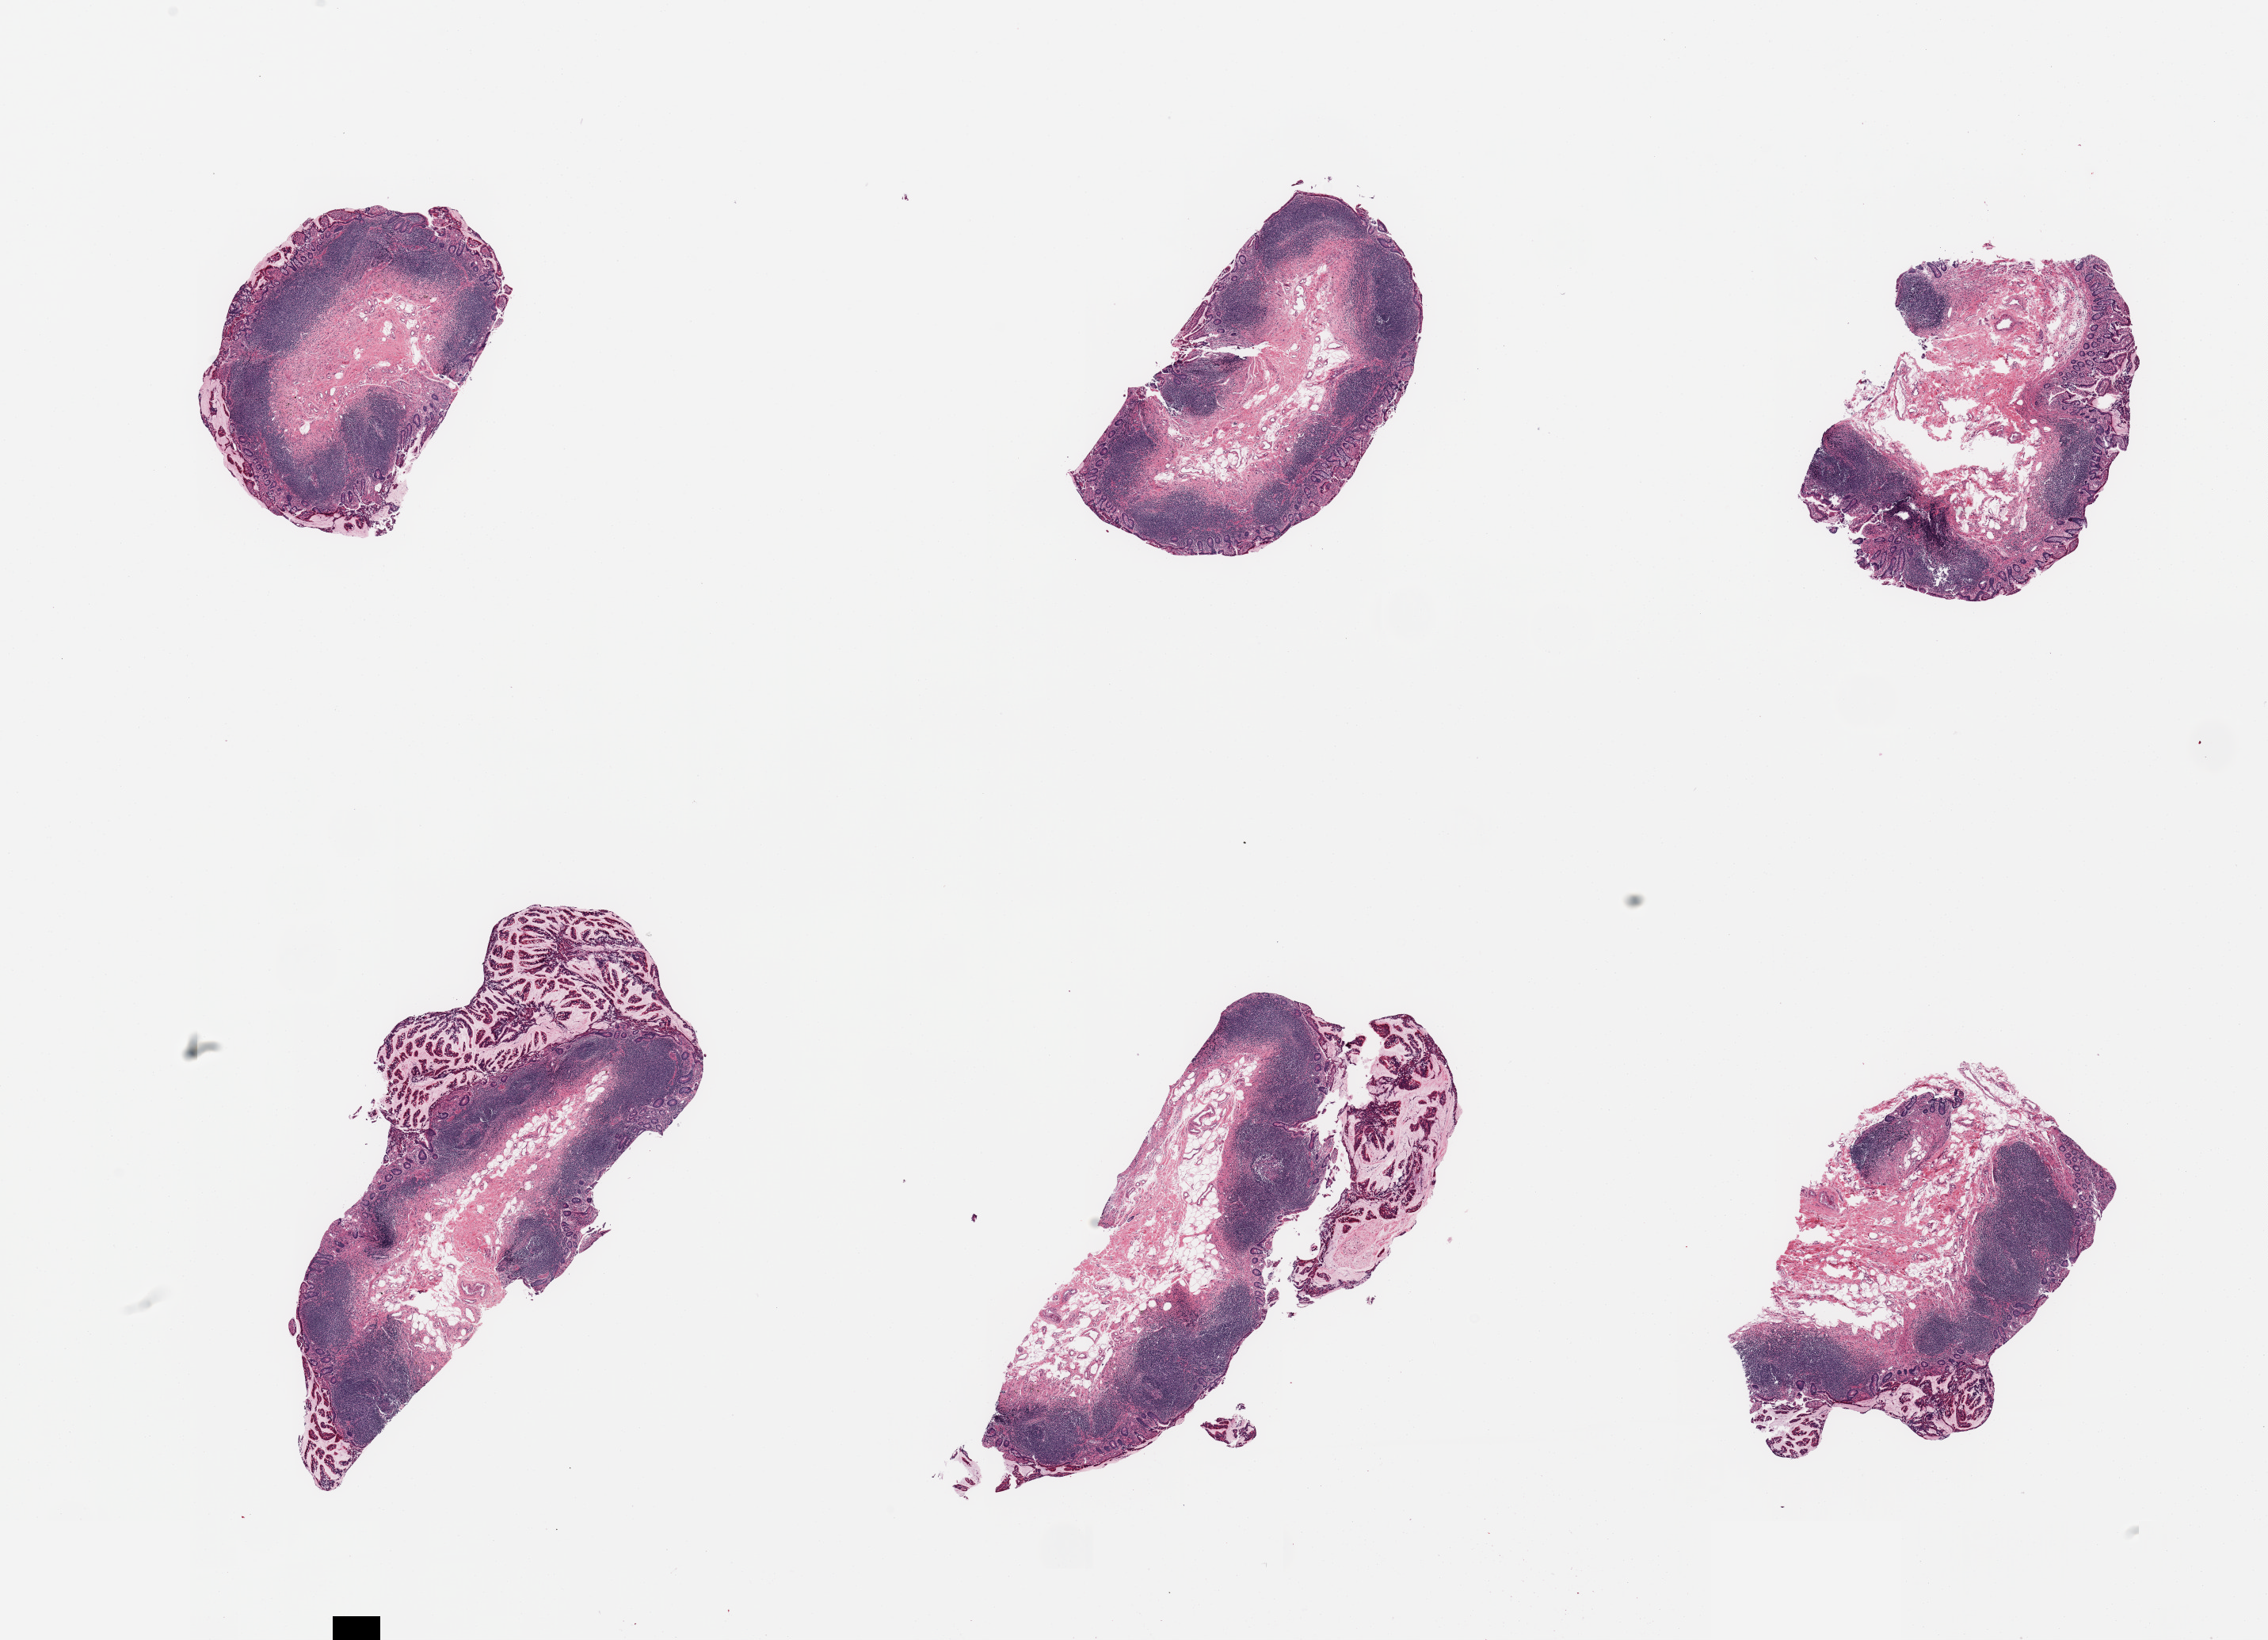
Digitized H&E-stained section, brightfield, low-resolution overview of the scanned area, about 22.6 x 16.4 mm (acquisition: 20x scan), PAXgene-fixed paraffin-embedded (PFPE) section, target tissue: ileum, tissue donor sample.
* pathologist's review note for this sample: 6 pieces; mucosa and submucosa with abundance of target lymphoid aggregates